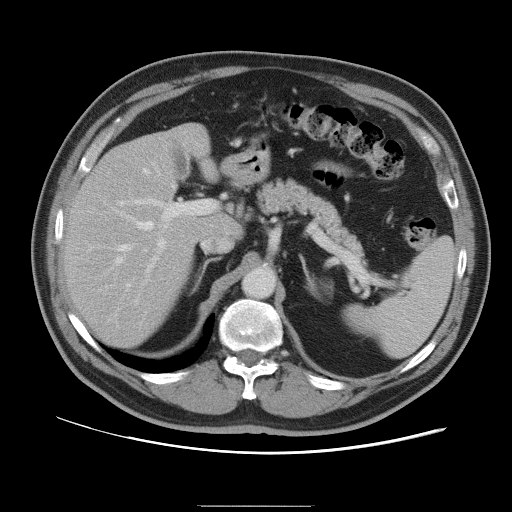
Contrast-enhanced abdominal CT, one axial slice. Slice 62 of 105 in the series (ordered by position). 120 kVp. Intravenous contrast given. Soft-tissue window (W 400 / L 40 HU). 5 mm slice thickness. 512 × 512 image matrix. Male patient, age 64 years. Case-level facts recorded for this patient, not image findings: diagnosis: colorectal cancer liver metastases, imaged before liver resection; multiple liver metastases: yes; largest metastasis: 3 cm; disease in both lobes: yes.
Annotated regions visible in this slice (manually delineated by an expert):
- hepatic veins: bounding box [x1, y1, x2, y2] px = [119, 169, 154, 286]
- liver: [64, 124, 239, 347]
- planned liver remnant (the part of the liver to remain after resection): [64, 135, 240, 348]
- portal vein (with intrahepatic branches): [115, 198, 193, 318]